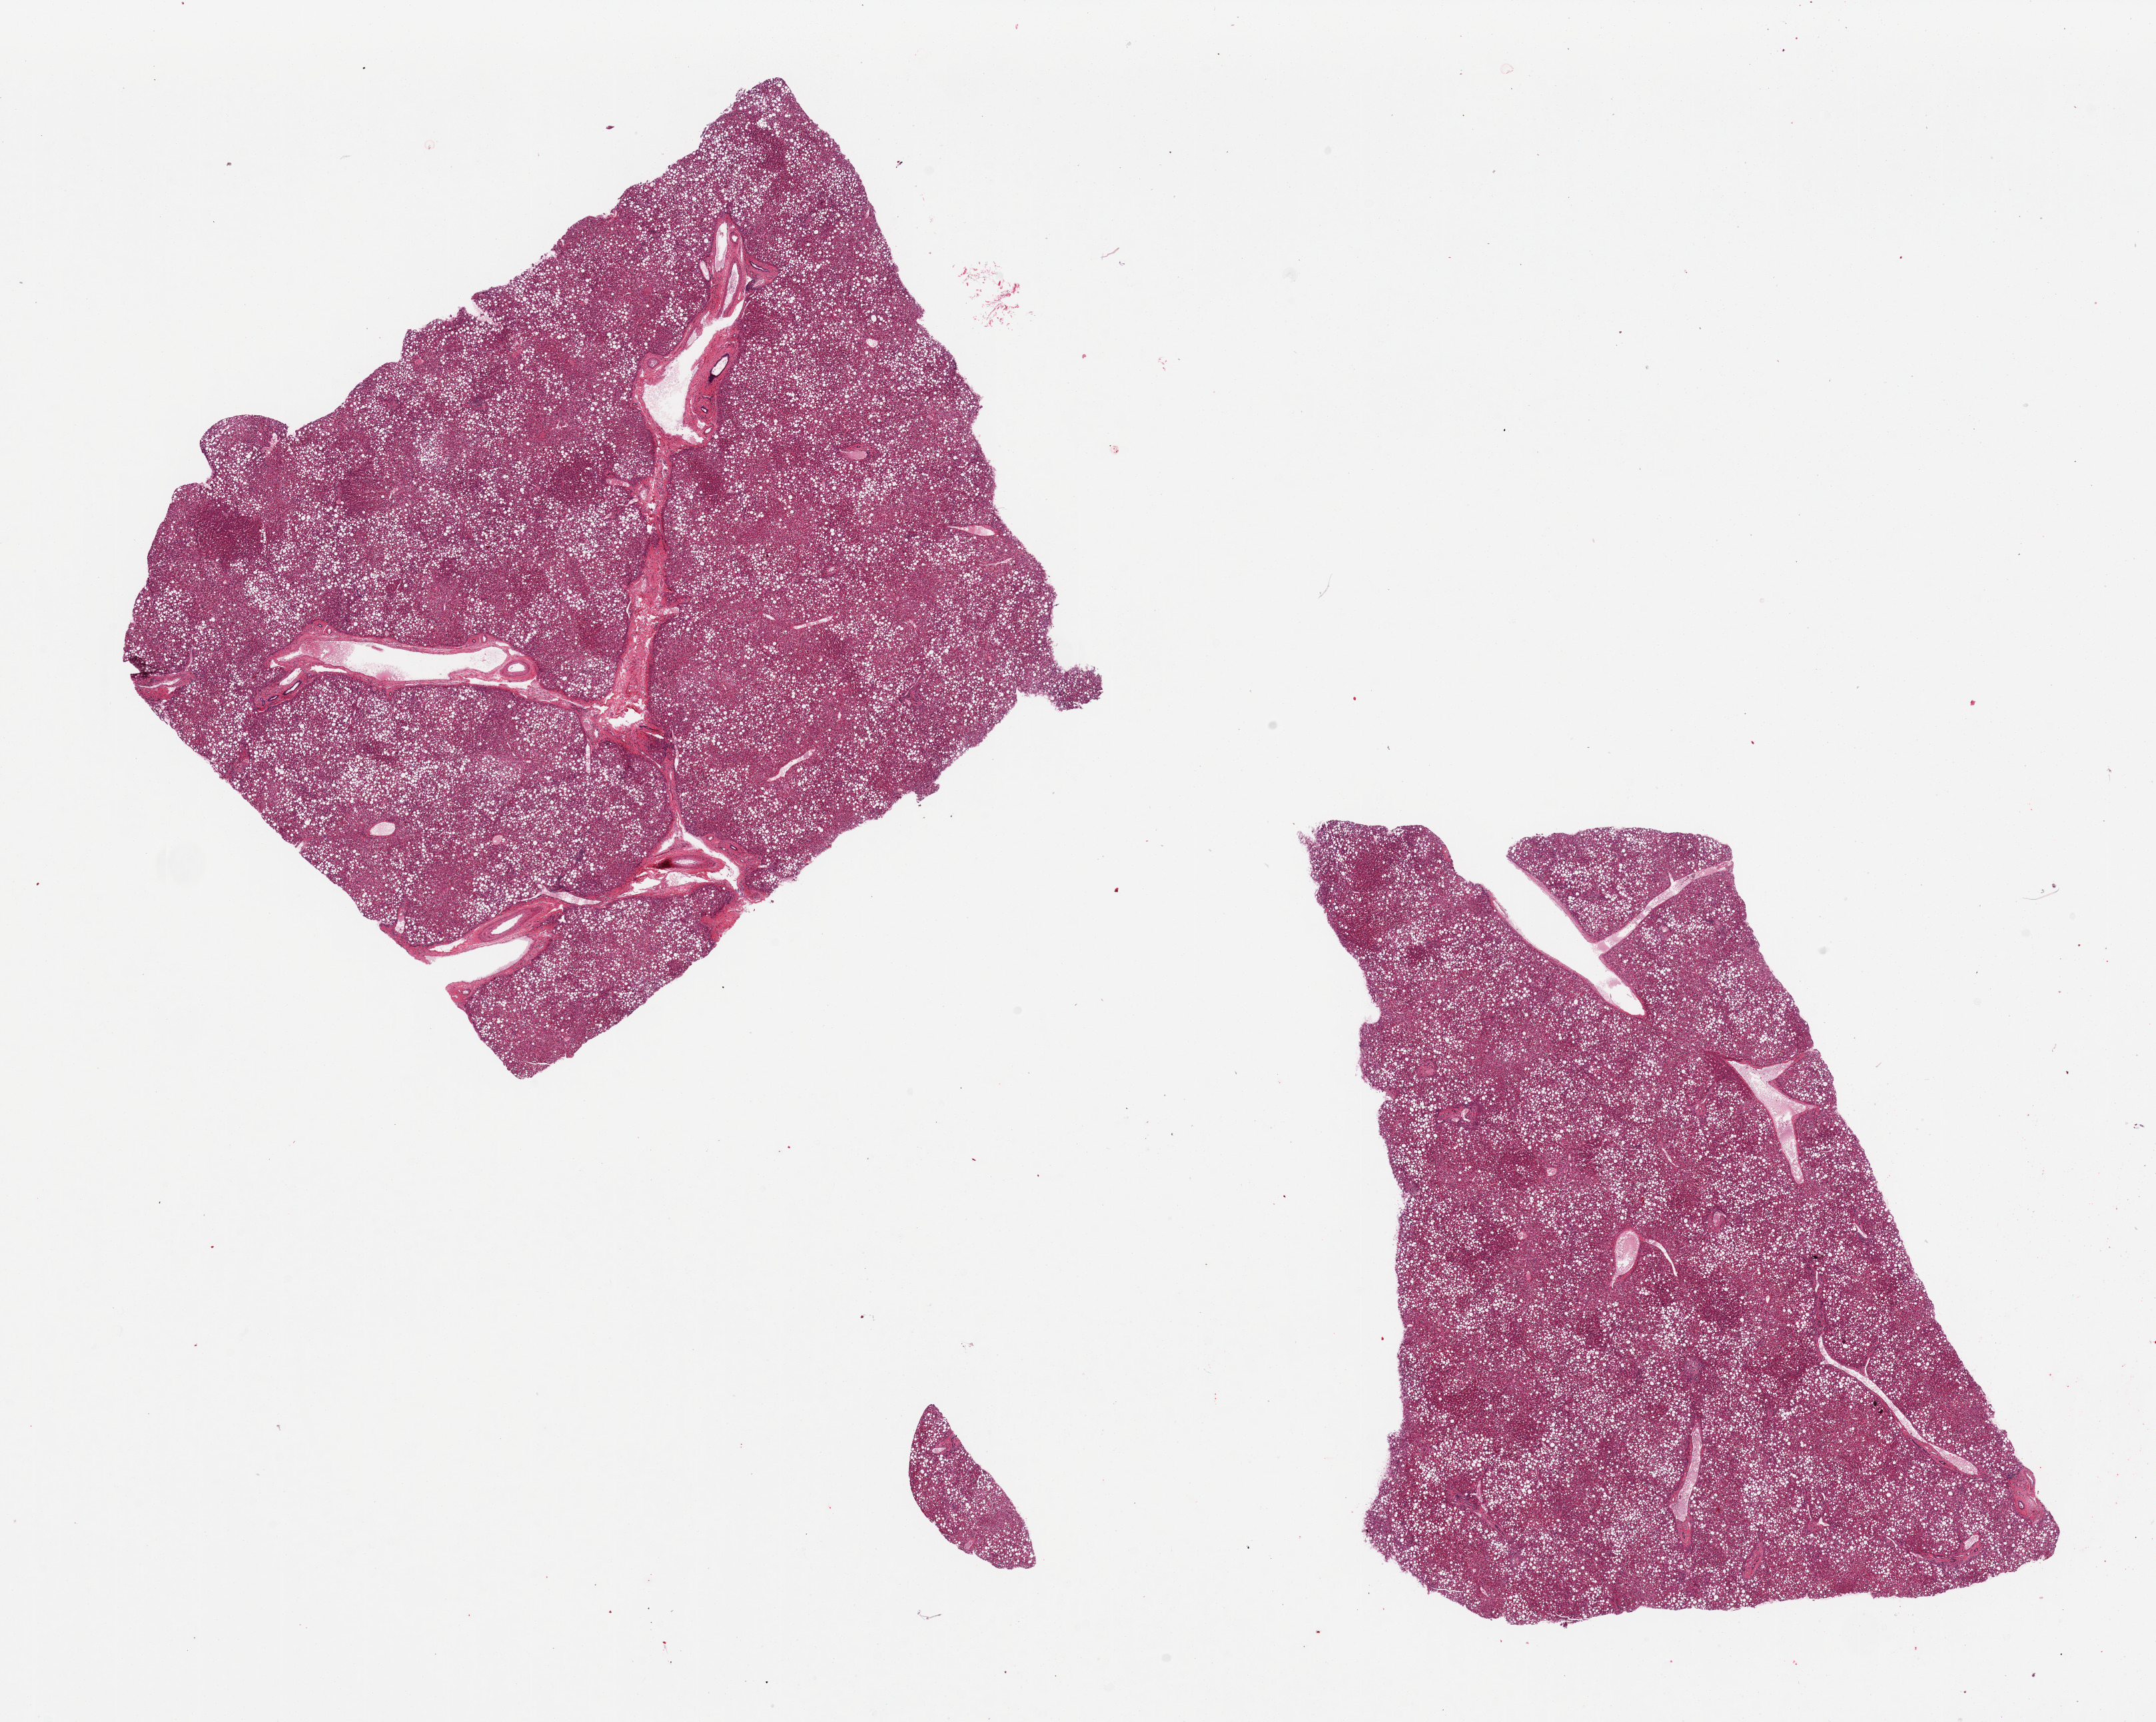
Digitized H&E-stained section — whole scanned area (about 25.6 x 20.4 mm, acquisition: 20x scan) shown as a low-resolution overview. PAXgene-fixed, paraffin-embedded tissue. Target tissue: liver. Donor tissue sample. Donor sex: female.
Pathologist's review note for this sample: 2 pieces; diffuse severe microvesicular and macrovesicular steatosis (~80%).